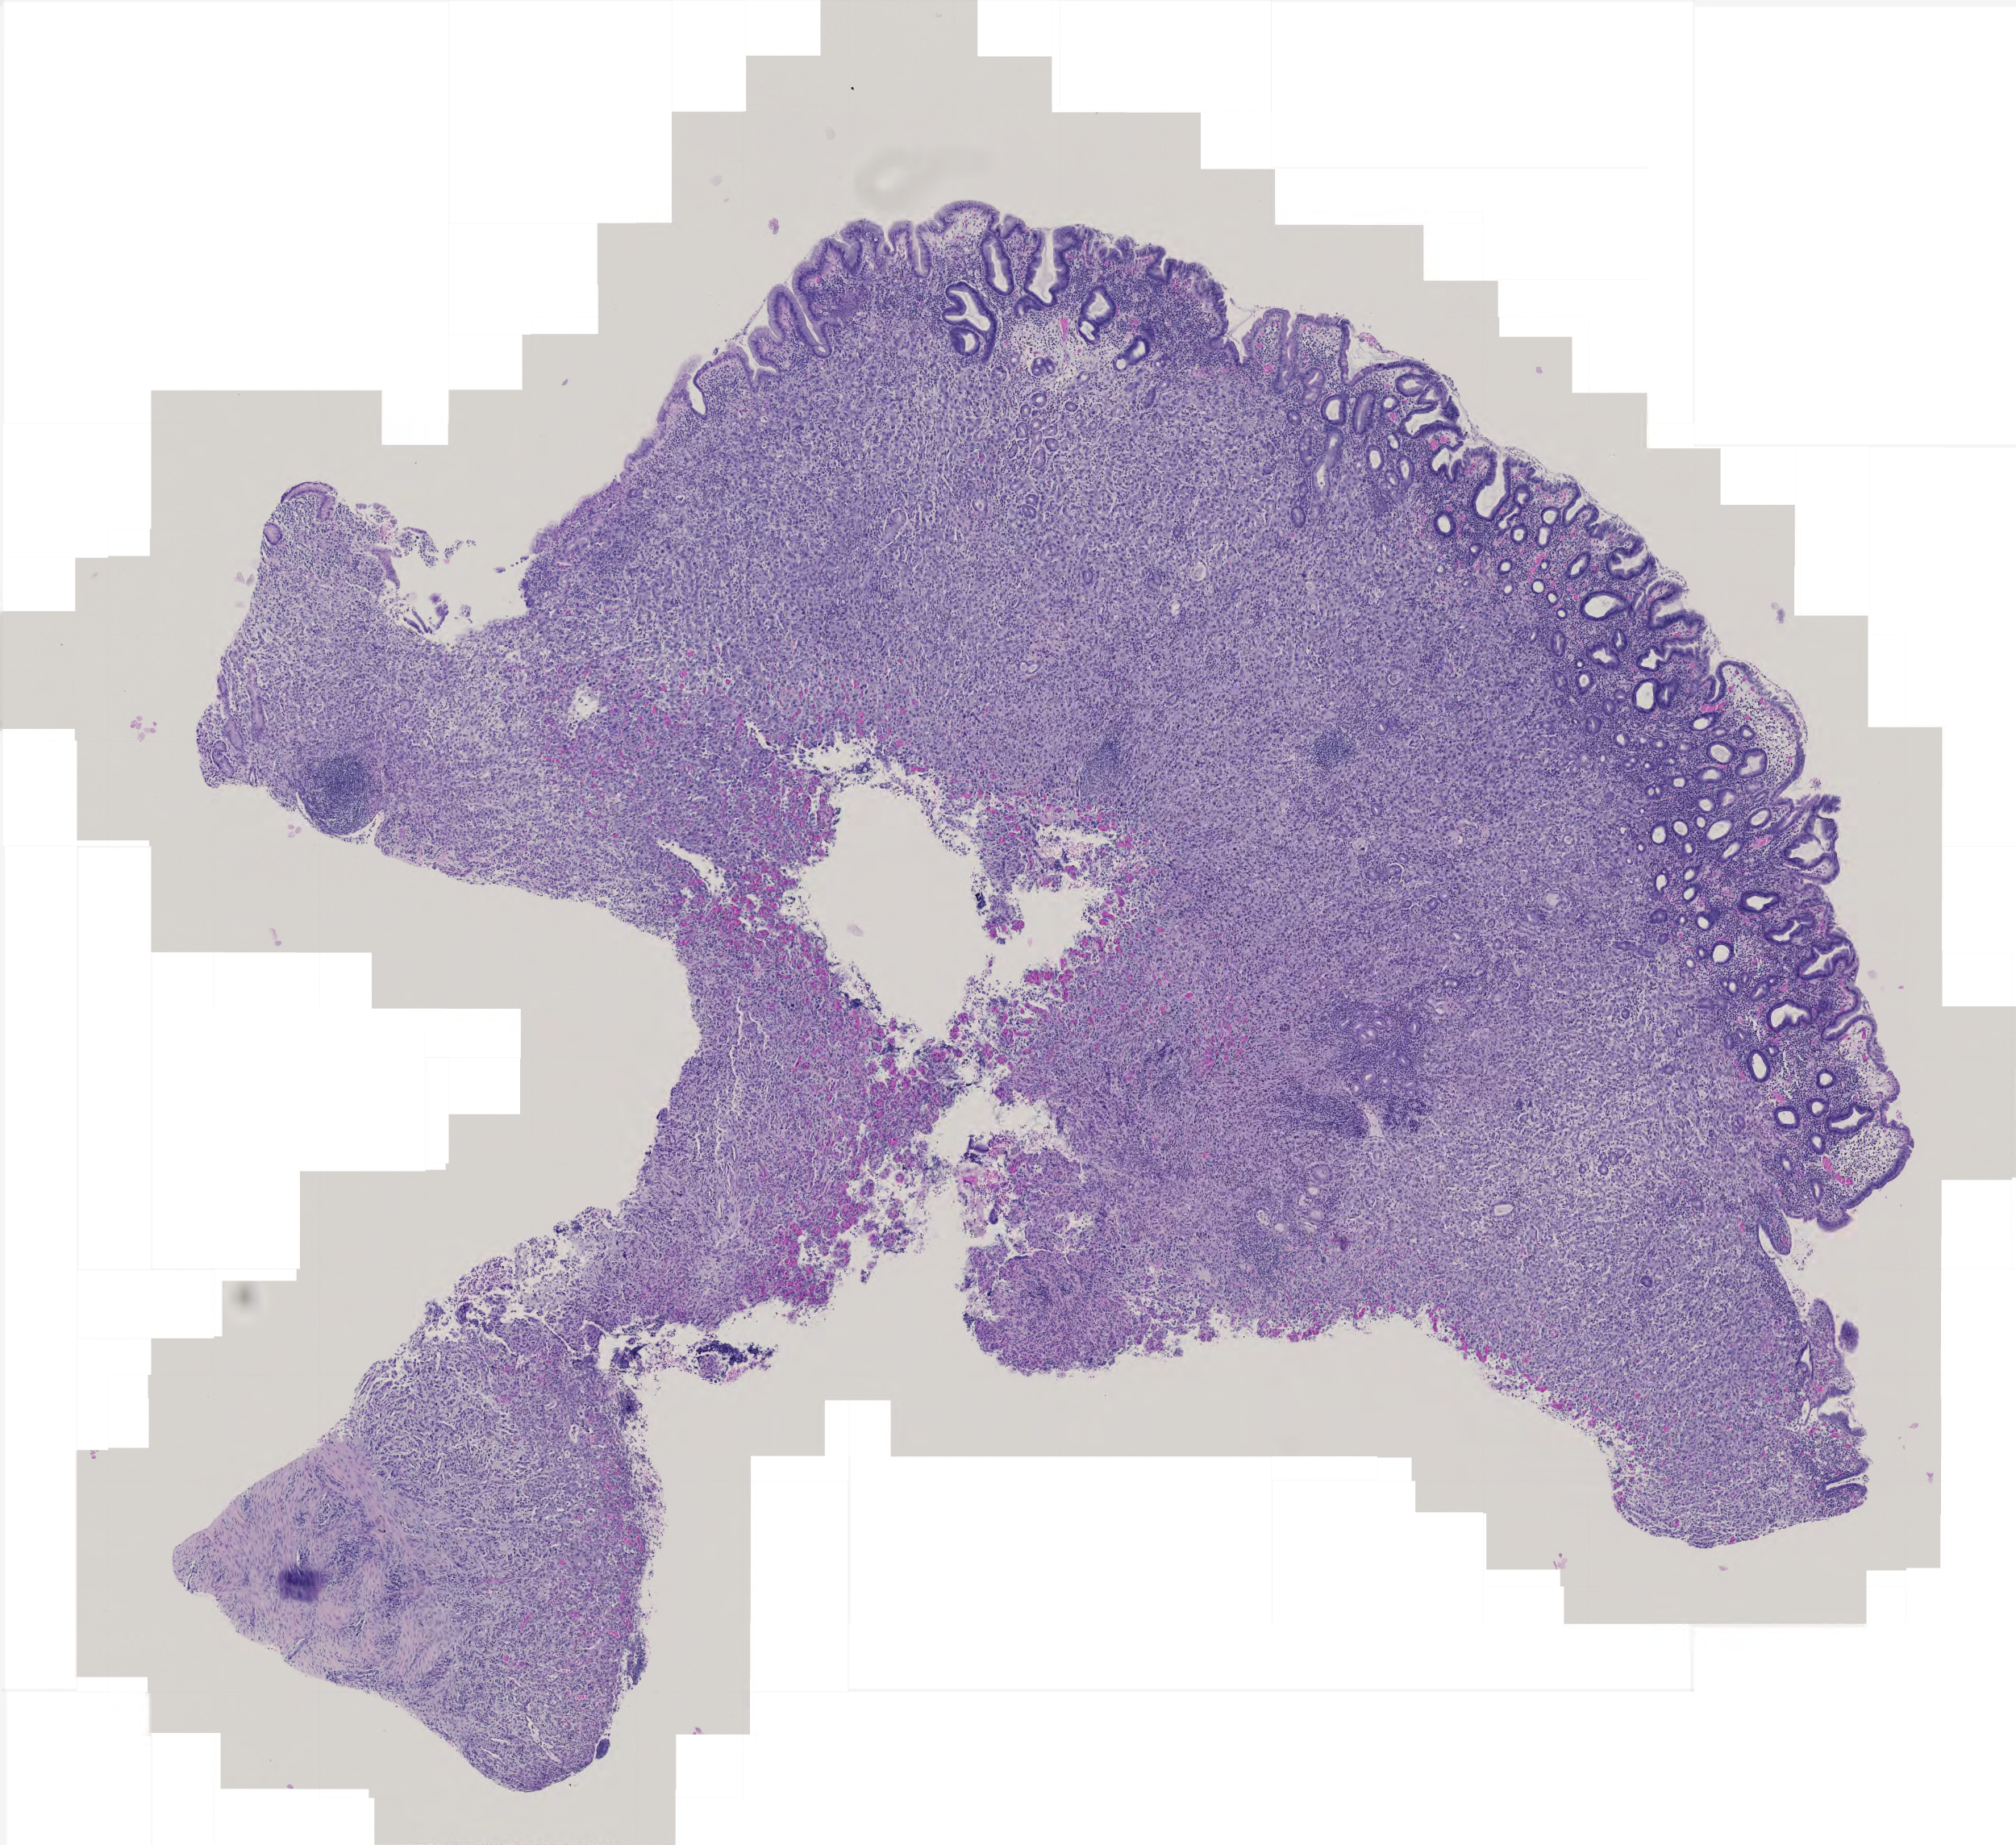
Digitized Hematoxylin and eosin (H&E) stained tissue section (whole slide) — whole scanned area (about 5.0 x 4.6 mm) shown as a low-resolution overview. Formalin-fixed paraffin-embedded (FFPE) diagnostic section. Stomach, primary tumour sample. Patient: male, age at initial diagnosis 85 years. Histologic grade: G2 (moderately differentiated).
Histologic diagnosis: Adenocarcinoma, NOS. AJCC pathologic stage: IV.